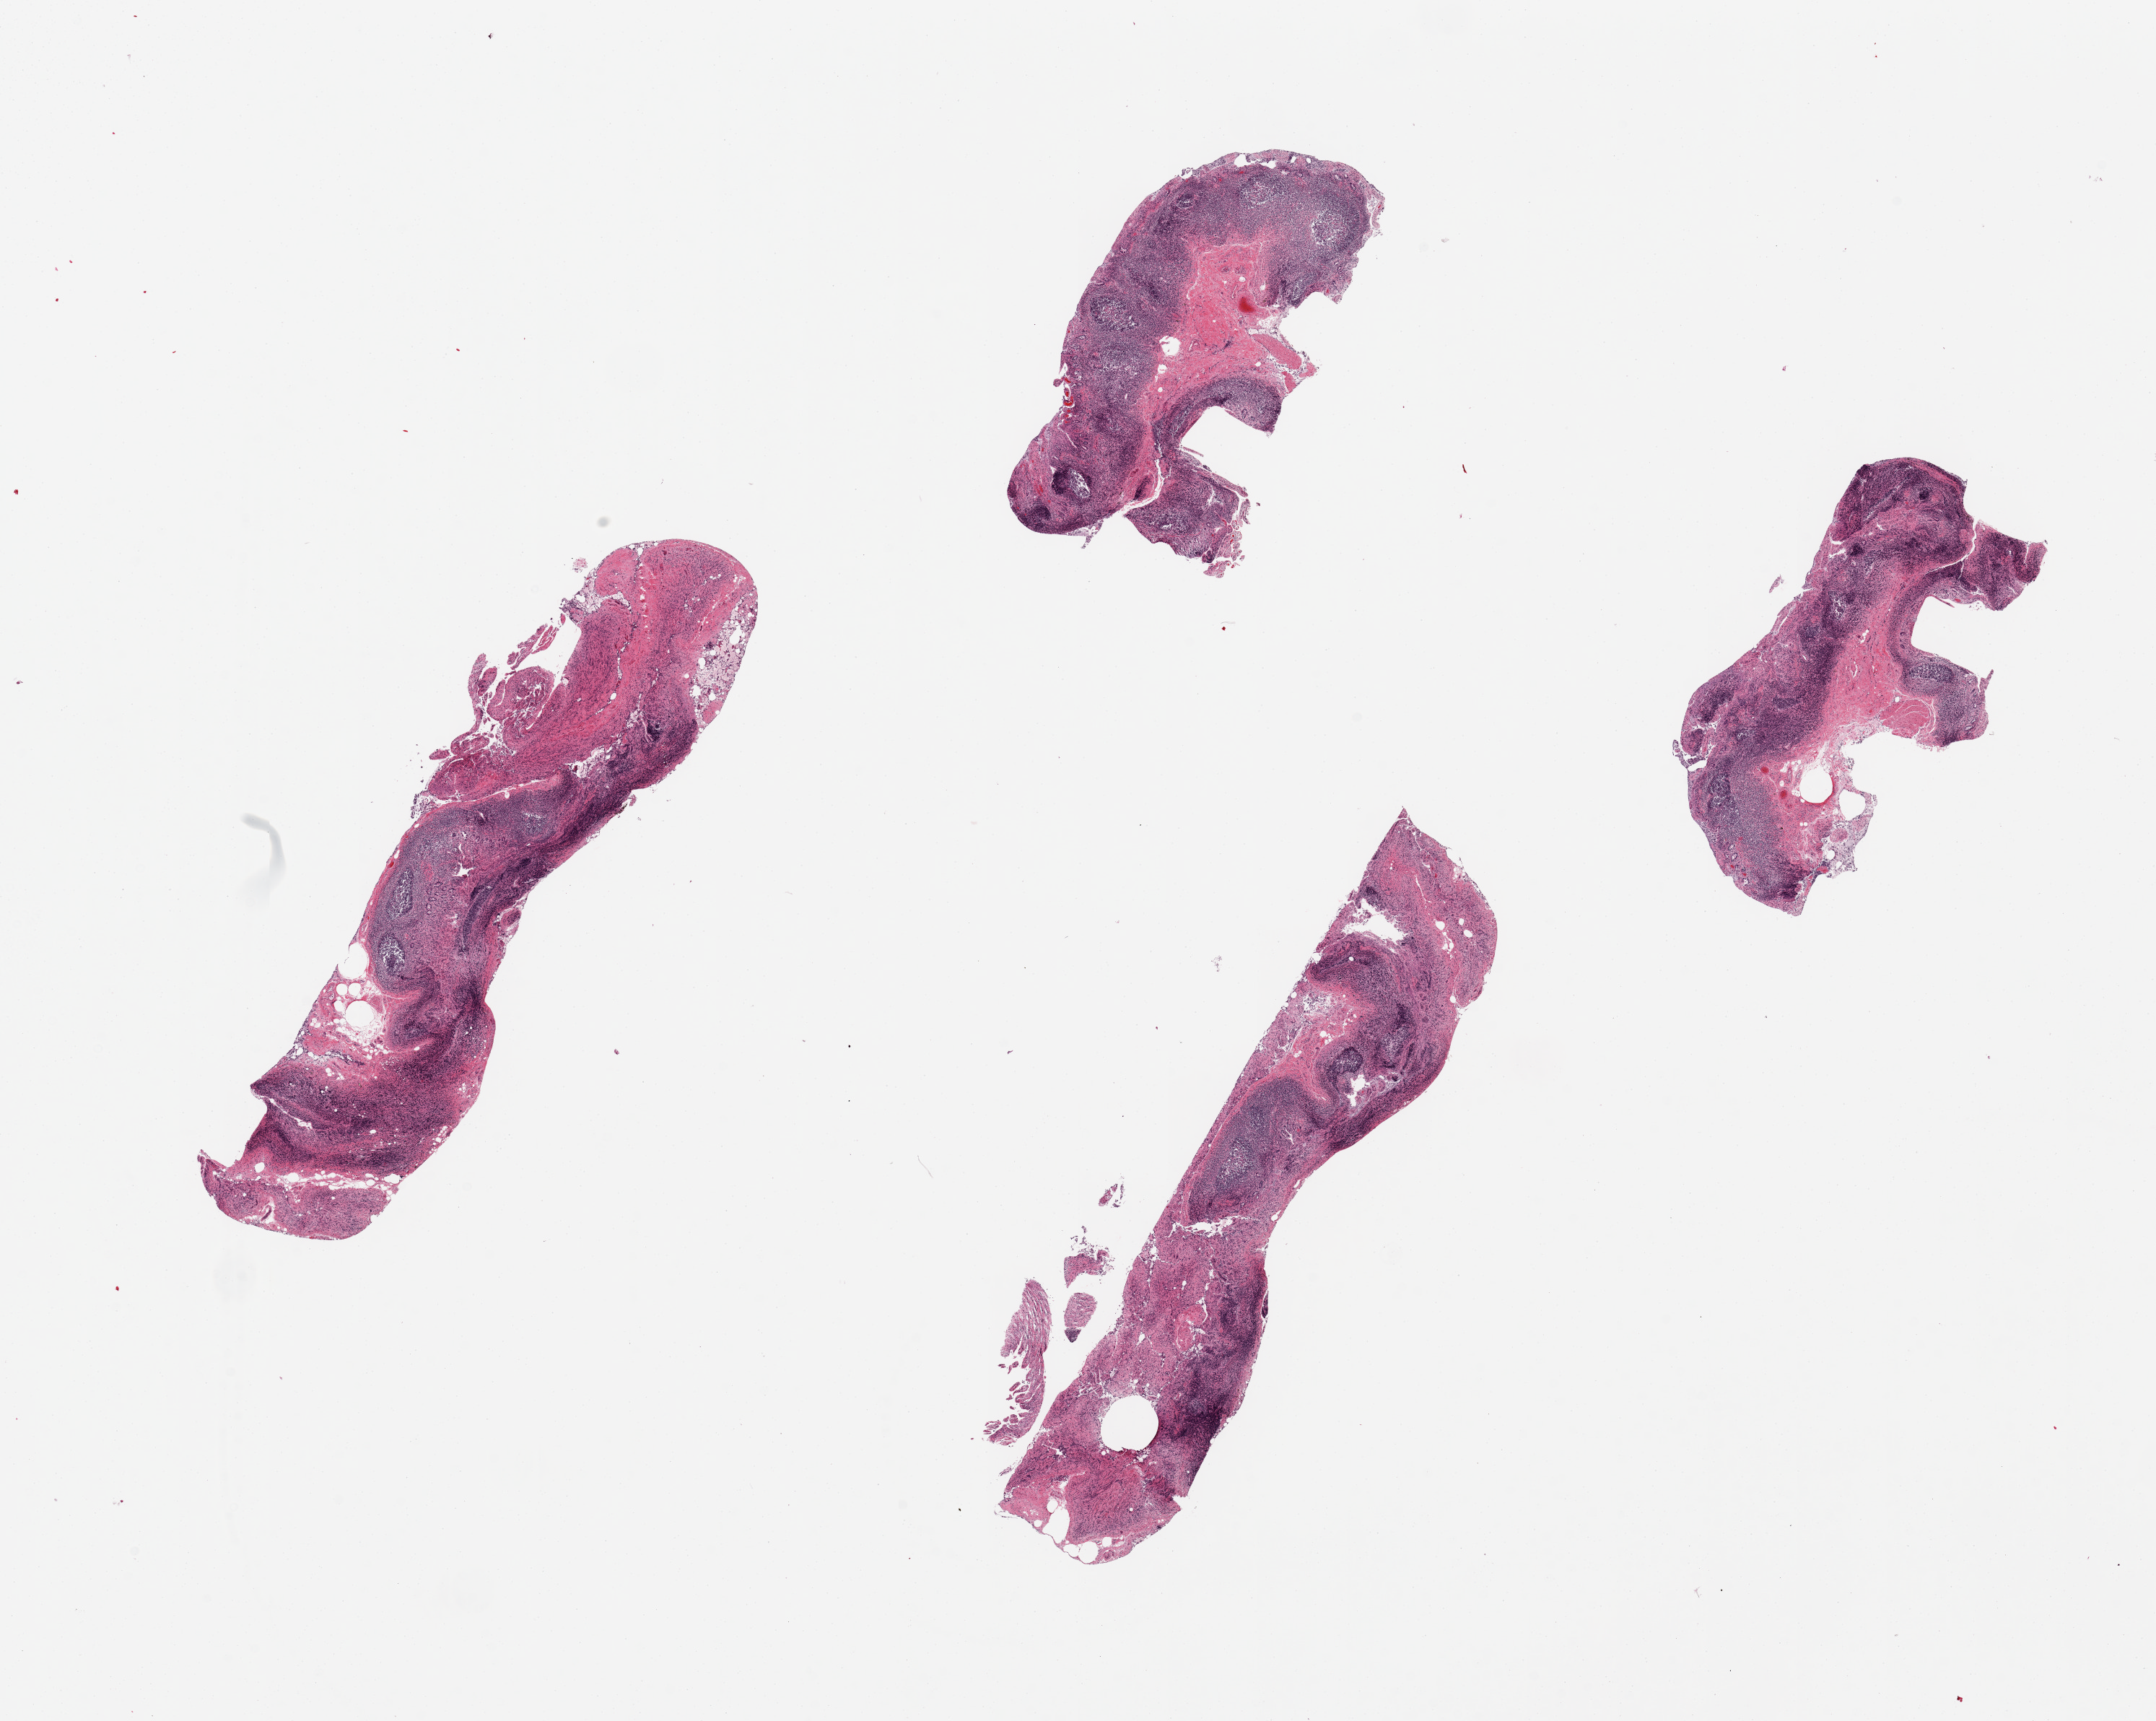
Digitized hematoxylin and eosin (H&E)-stained section, whole scanned area (about 23.6 x 18.9 mm, slide scanned at 20x) shown as a low-resolution overview. PAXgene-fixed, paraffin-embedded tissue. Target tissue: ileum. Donor tissue sample.
Pathologist's review note for this sample: 4 pieces, ~40% lymphoid aggregates but badly autolyzed.